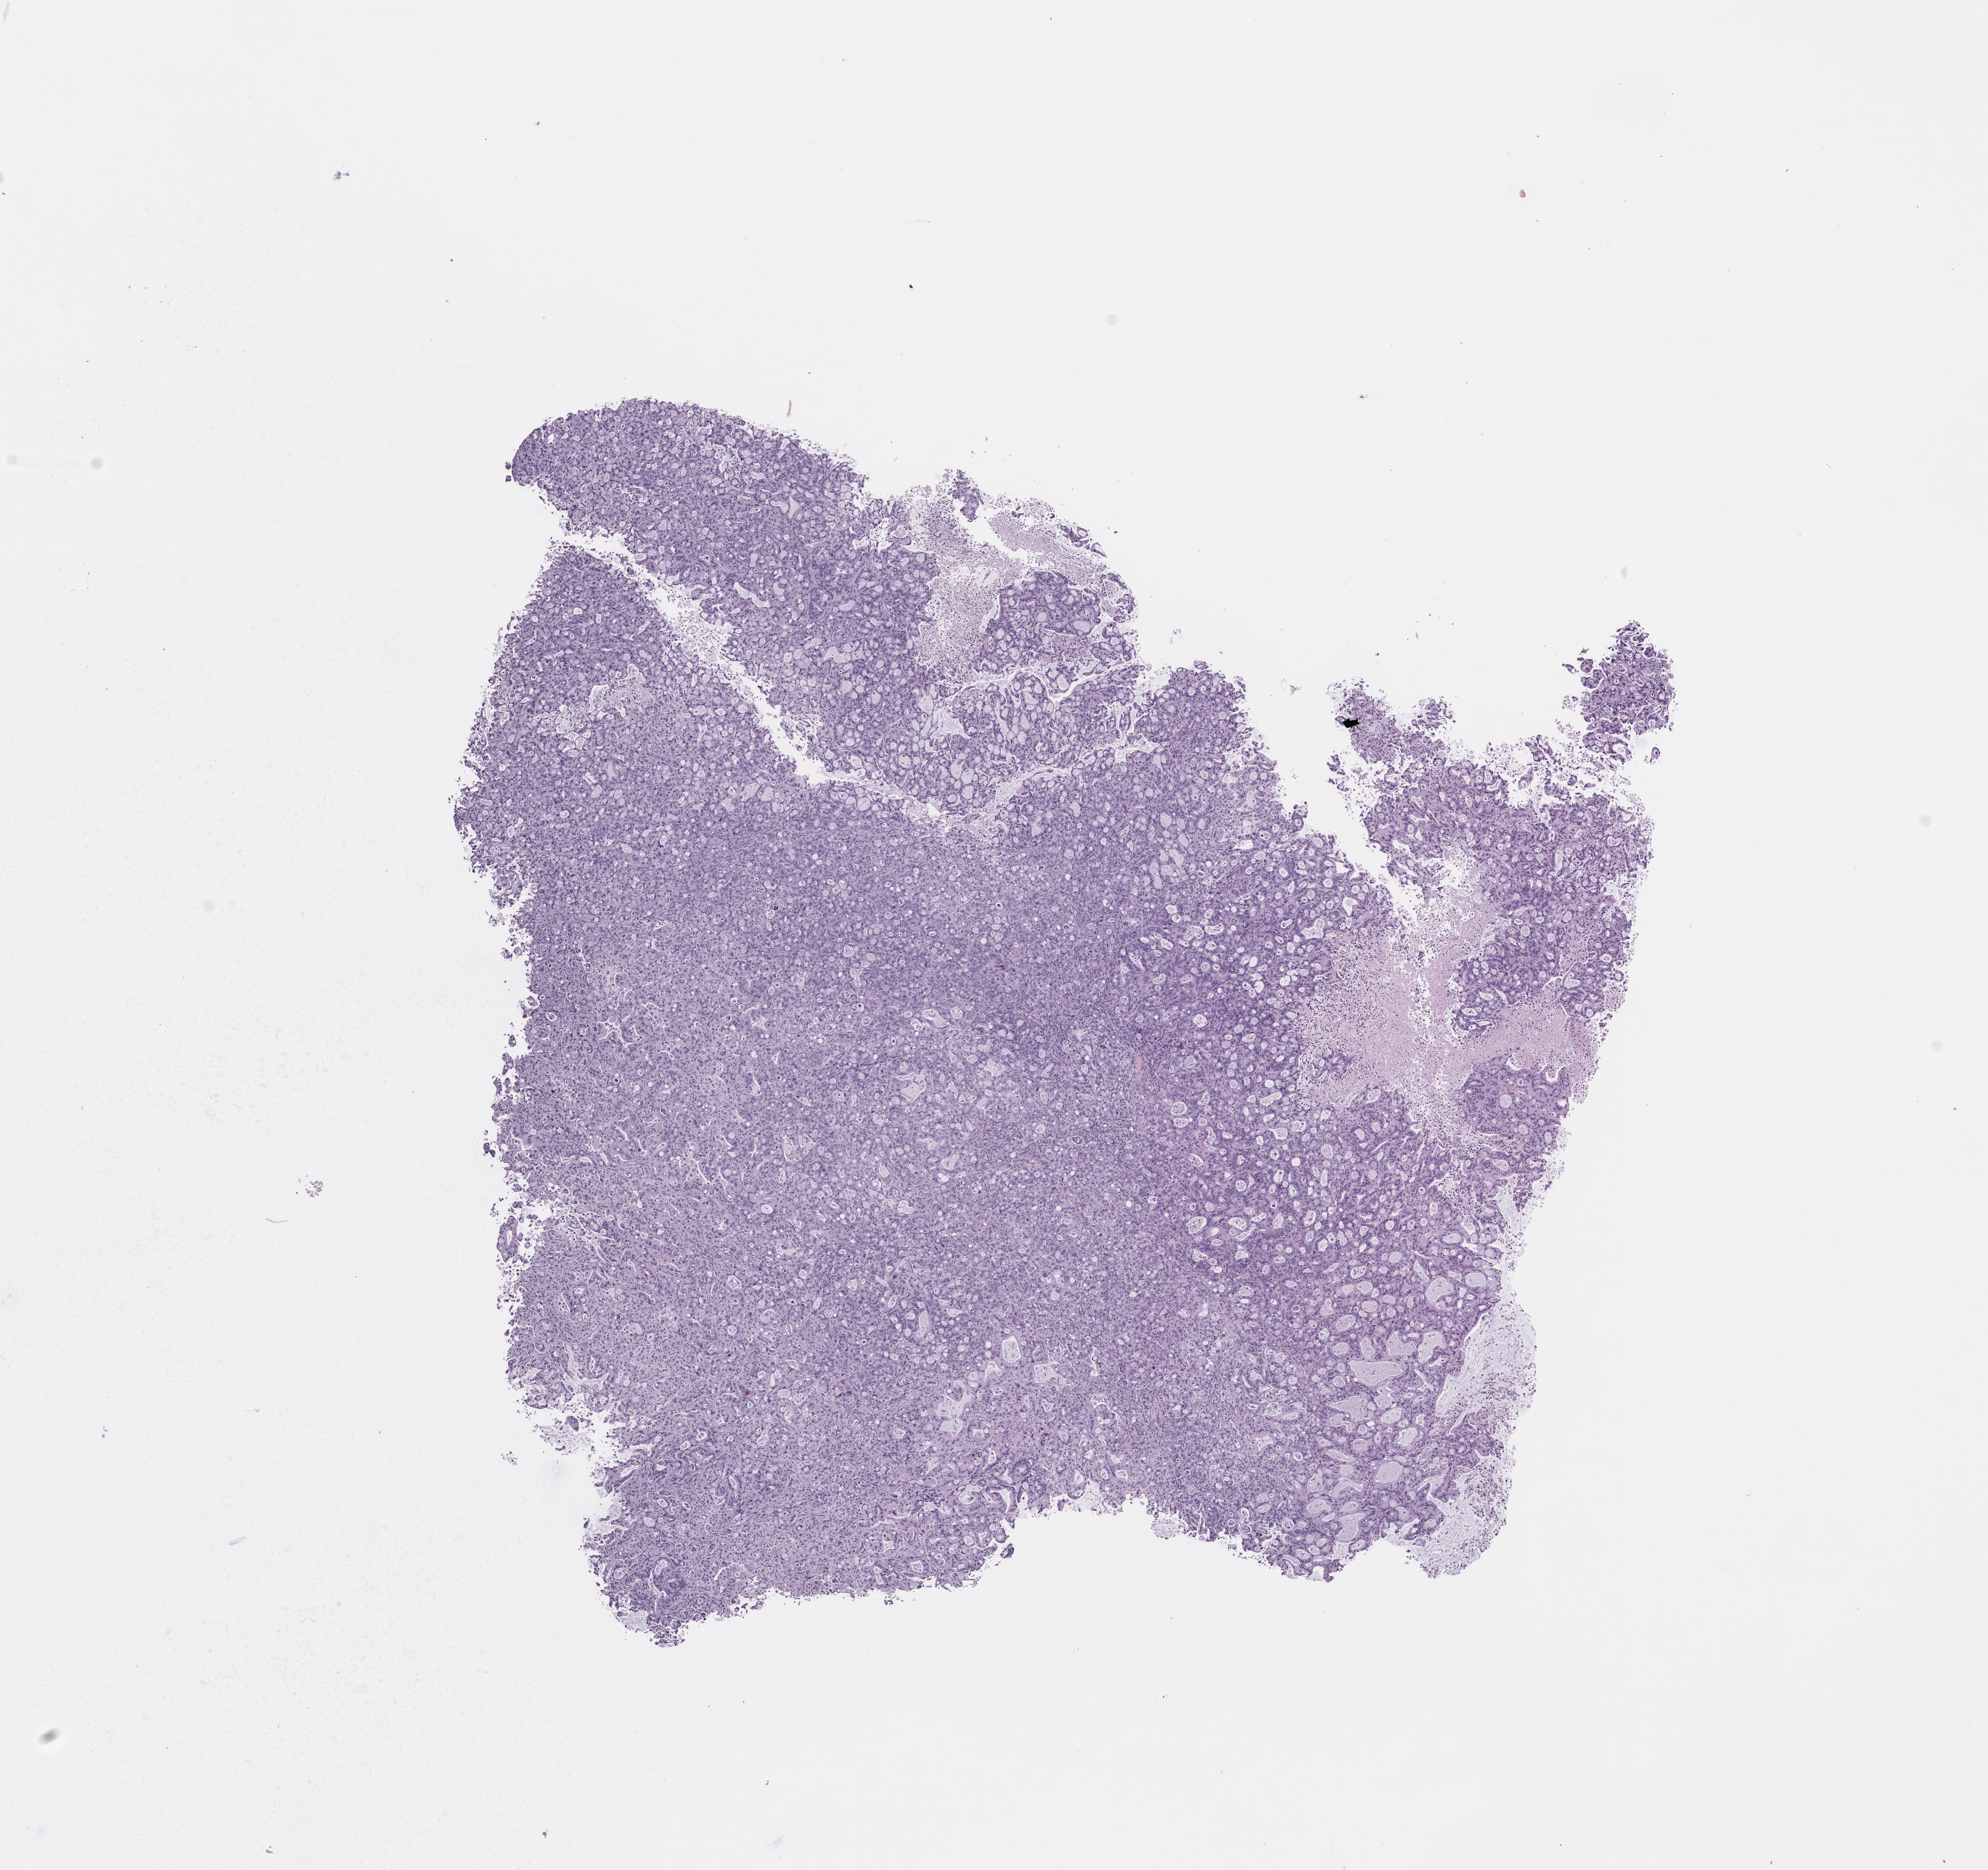
Whole-slide image, haematoxylin and eosin: patient-derived xenograft (human tumor grown in a mouse), a low-resolution overview of the entire scanned area, about 11.0 x 10.4 mm, formalin-fixed, paraffin-embedded (FFPE) tissue, tumor site category: pancreas.
Originating patient diagnosis: Pancreatic Adenocarcinoma.